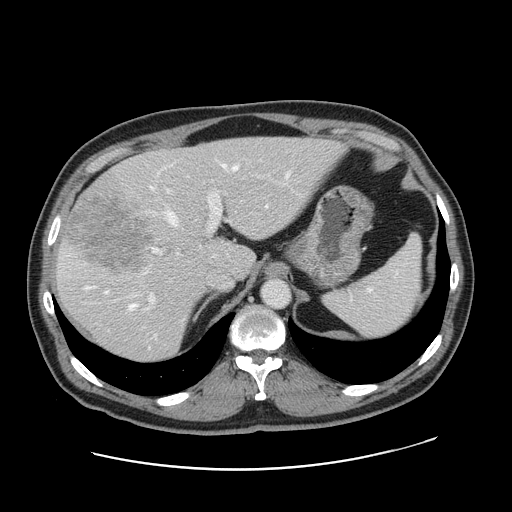
Contrast-enhanced abdominal CT, one axial slice. Slice 117 of 178 in the series (ordered by position). 120 kVp. Intravenous contrast given. Soft-tissue window (W 400 / L 40 HU). 2.5 mm slice thickness. 512 × 512 image matrix, field of view 403 × 403 mm. Male patient, age 63 years. From the clinical record (not read from this slice): diagnosis: colorectal cancer liver metastases, imaged before liver resection; multiple liver metastases: yes; largest metastasis: 8 cm; disease in both lobes: yes.
Outlined on this slice (expert manual segmentation):
- hepatic veins: bounding box (x1, y1, x2, y2) in pixels: (86, 164, 290, 310)
- liver: (56, 138, 342, 363)
- planned liver remnant (the part of the liver to remain after resection): (139, 138, 342, 277)
- portal vein (with intrahepatic branches): (144, 175, 269, 310)
- liver metastasis: (65, 195, 152, 278)